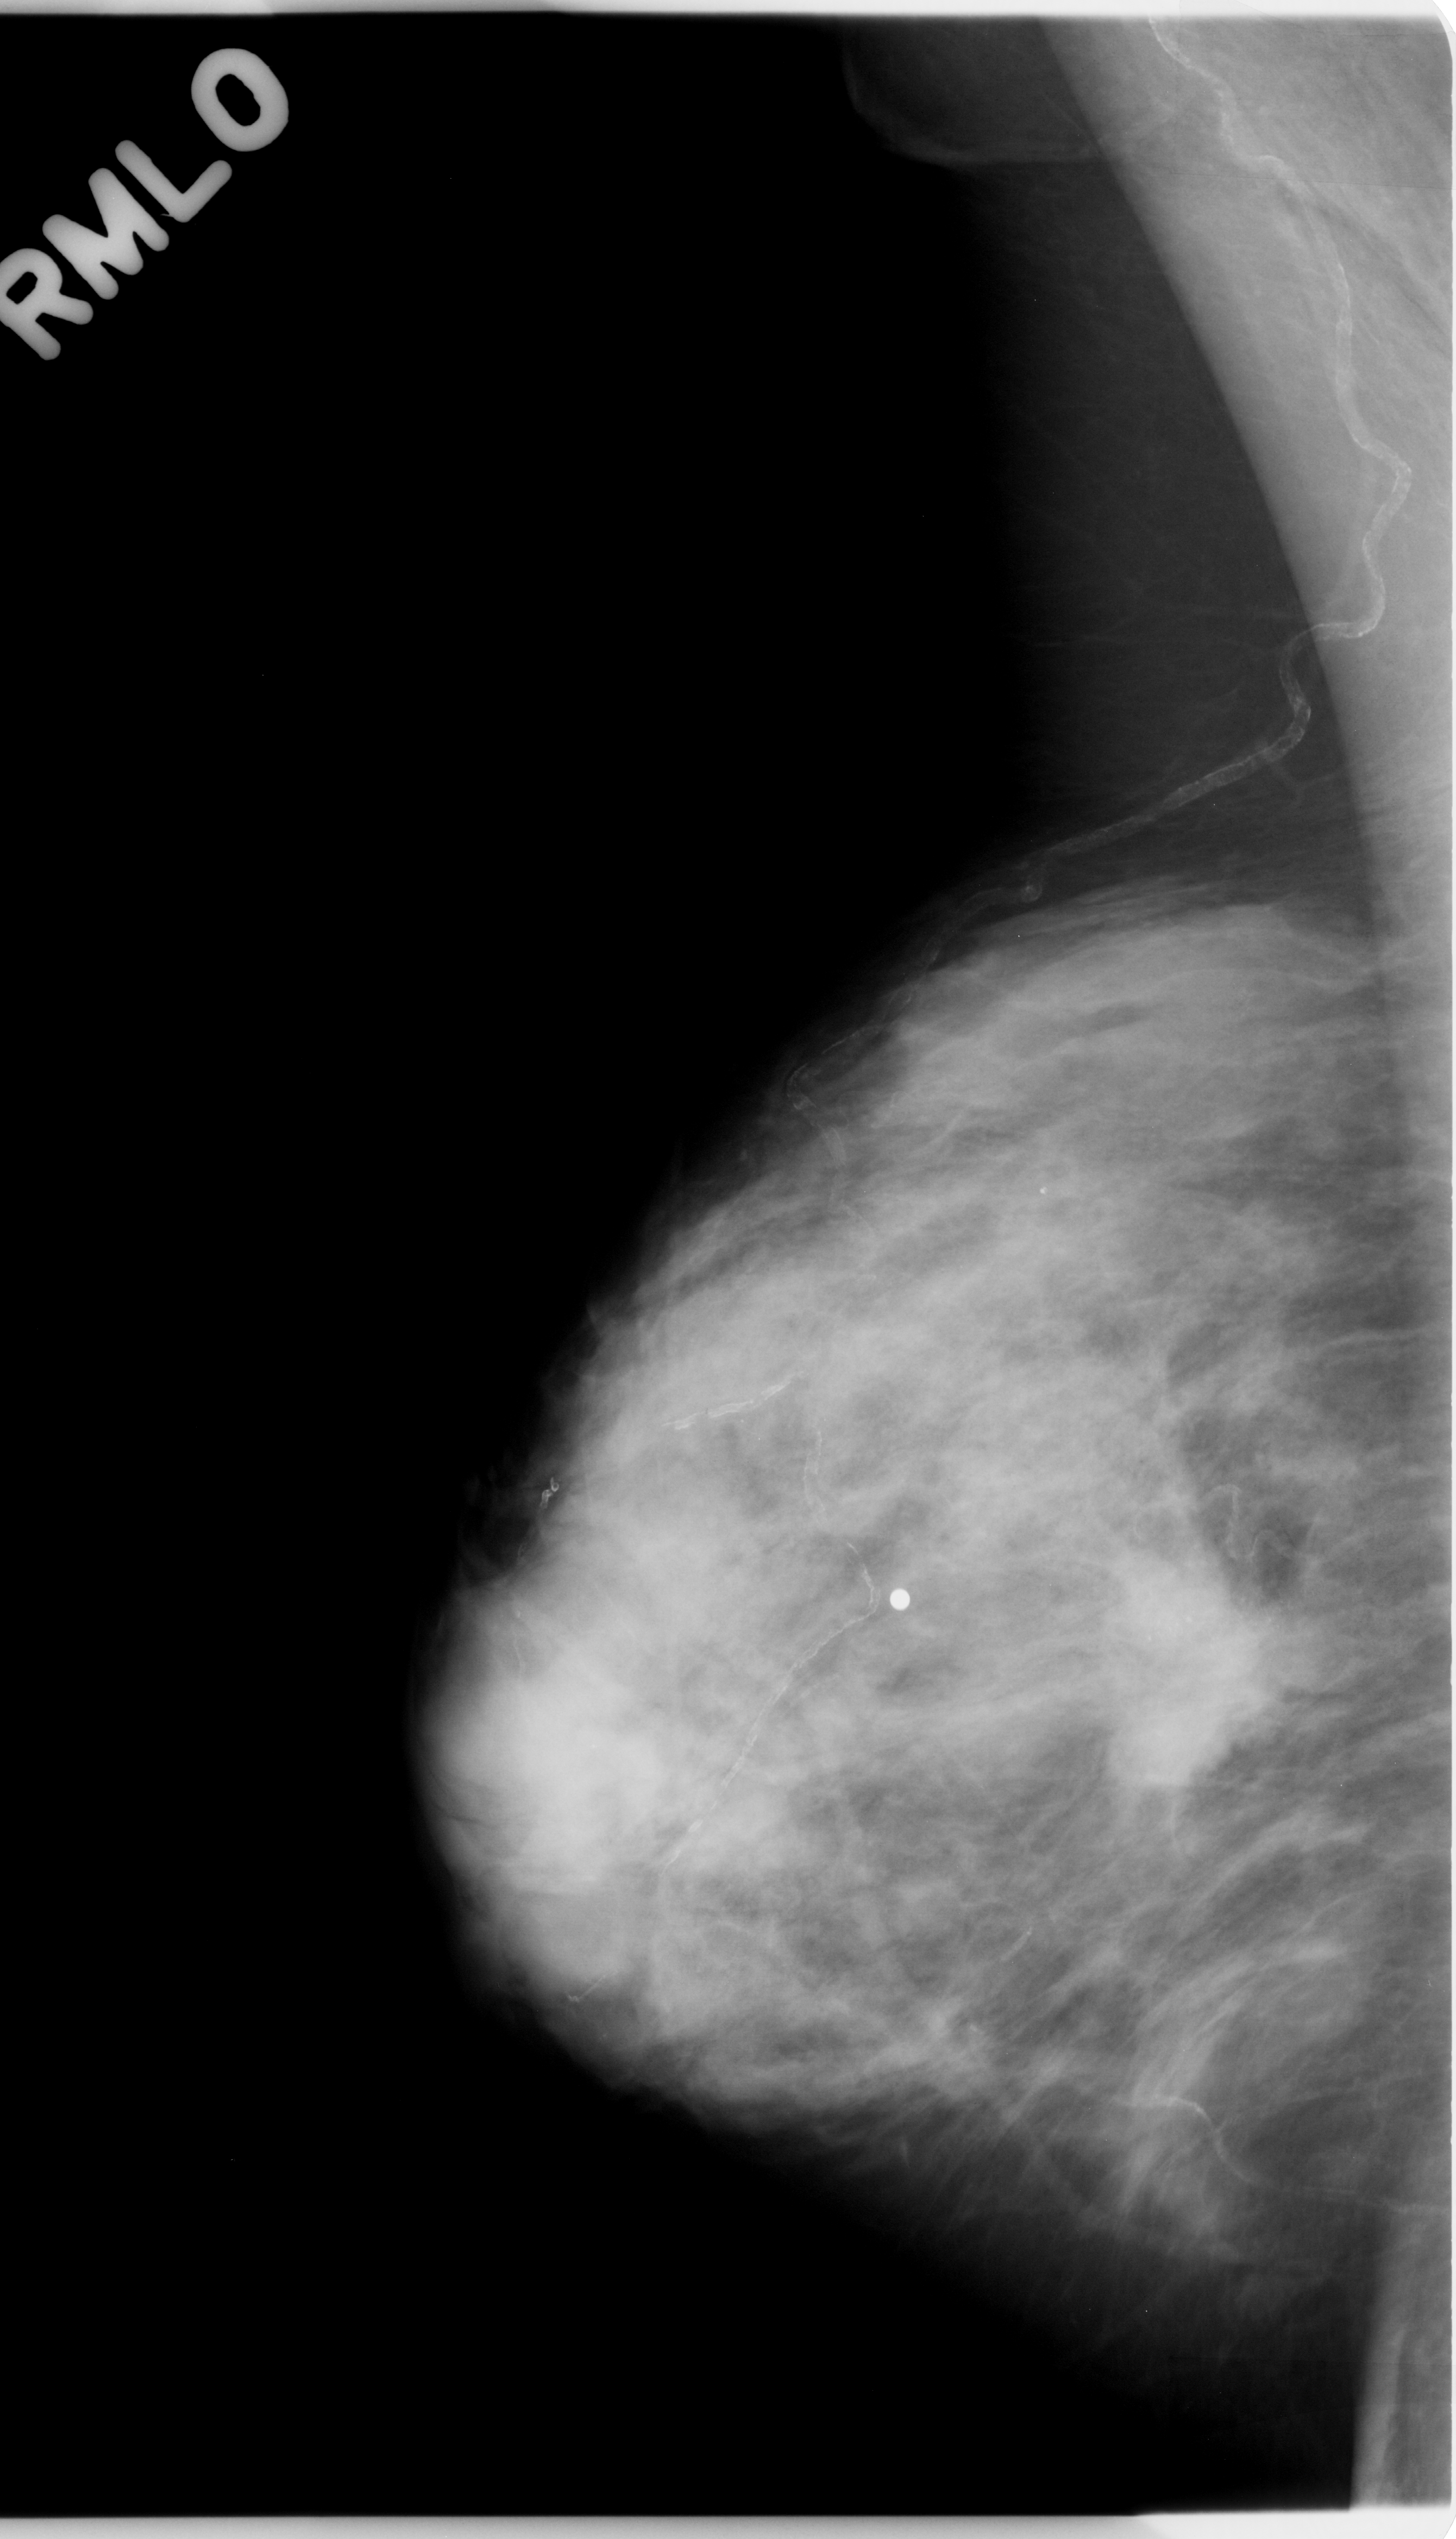
Scanned film-screen mammogram, right breast, MLO view, breast composition: heterogeneously dense (BI-RADS density category 3 of 4).
Calcifications, morphology amorphous, distribution clustered; BI-RADS assessment category 5; pathology (as recorded): malignant.